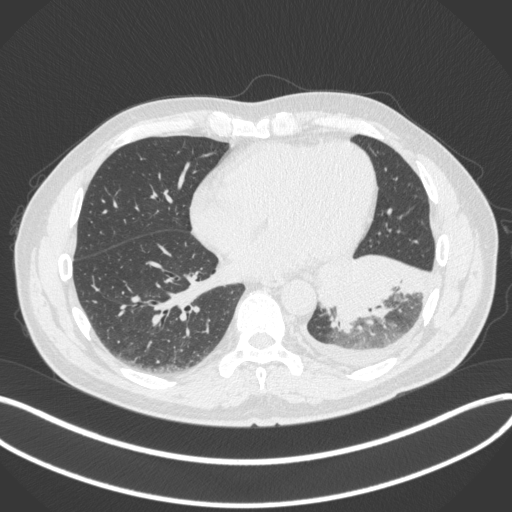
Chest CT, one axial slice. Position 130 of 350 along the scan axis. Lung window (W 1500 / L -600 HU). 1 mm slice thickness. 512 × 512 image matrix, field of view 400 × 400 mm. Patient: male, 58 years. From the clinical record (not read from this slice): clinical TNM (as recorded): T3 N1 M1b; histopathological grade: G3.
Annotated regions visible in this slice (rectangle marked by the reading radiologist):
- lung tumour (recorded histology: small cell carcinoma): bounding box [x1, y1, x2, y2] px = [323, 249, 436, 328]